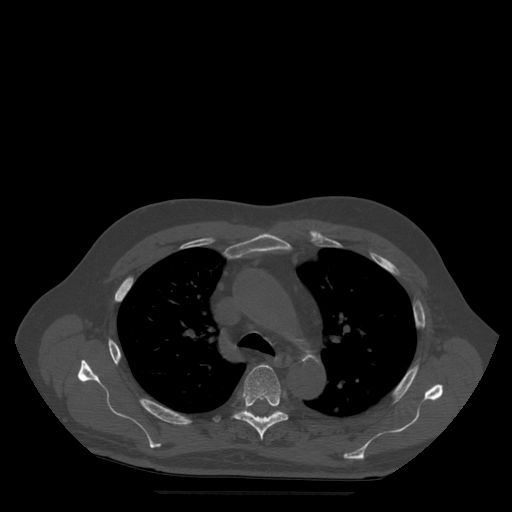
CT including the spine, one axial slice; position 372 of 522 along the scan axis; bone window (W 1800 / L 400 HU); 512 × 512 image matrix, field of view 420 × 420 mm. Patient age 72 years. Case-level facts recorded for this patient, not image findings: primary cancer: prostate.
Annotated regions visible in this slice (semi-automatic segmentation, software-assisted and operator-edited):
- T5 vertebra: bounding box (x1, y1, x2, y2) in pixels: (233, 365, 289, 441)
- T6 vertebra: (268, 413, 274, 418)